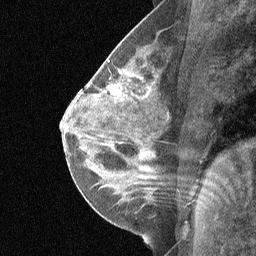
Breast MRI (dynamic contrast-enhanced), one sagittal slice. Position 33 of 64 along the scan axis. Dynamic contrast-enhanced study with each time point stored as its own series, time point 3 of 5 at this slice position (ordered by acquisition time). 1.5 T. TE 4.8 ms, TR 27 ms. 256 × 256 image matrix, field of view 180 × 180 mm. Patient: female, 26 years. Case-level facts recorded for this patient, not image findings: setting: breast cancer imaged before/during neoadjuvant chemotherapy; receptor status: HR-positive, HER2-negative.
Outlined on this slice (semi-automatically segmented with operator editing):
- analysis volume of interest (the breast-tissue region the enhancement analysis was run in; not a lesion): bounding box <85,46,169,144> (left, top, right, bottom; pixels)
- tumour enhancement mask (voxels above the 90 % enhancement threshold inside the analysis volume of interest): <110,87,120,95>